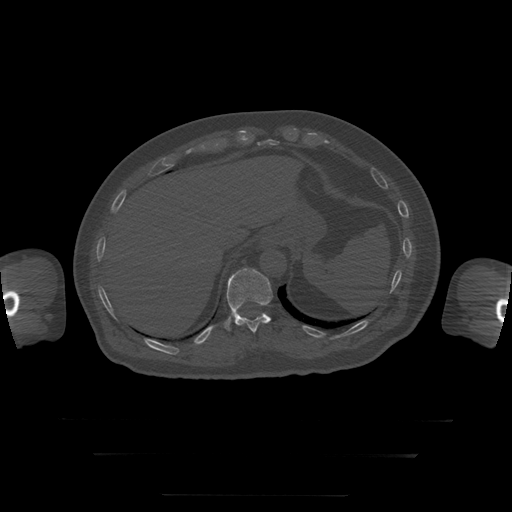
CT including the spine, one axial slice. Slice 99 of 397 in the series (ordered by position). Reconstruction kernel STANDARD. 120 kVp. Bone window (W 1800 / L 400 HU). 1.25 mm slice thickness. 512 × 512 image matrix, field of view 510 × 510 mm. Patient age 73 years. From the clinical record (not read from this slice): primary cancer: prostate.
Structures marked on this image (semi-automatic segmentation, software-assisted and operator-edited):
- T11 vertebra: bounding box <224,268,273,333> (left, top, right, bottom; pixels)